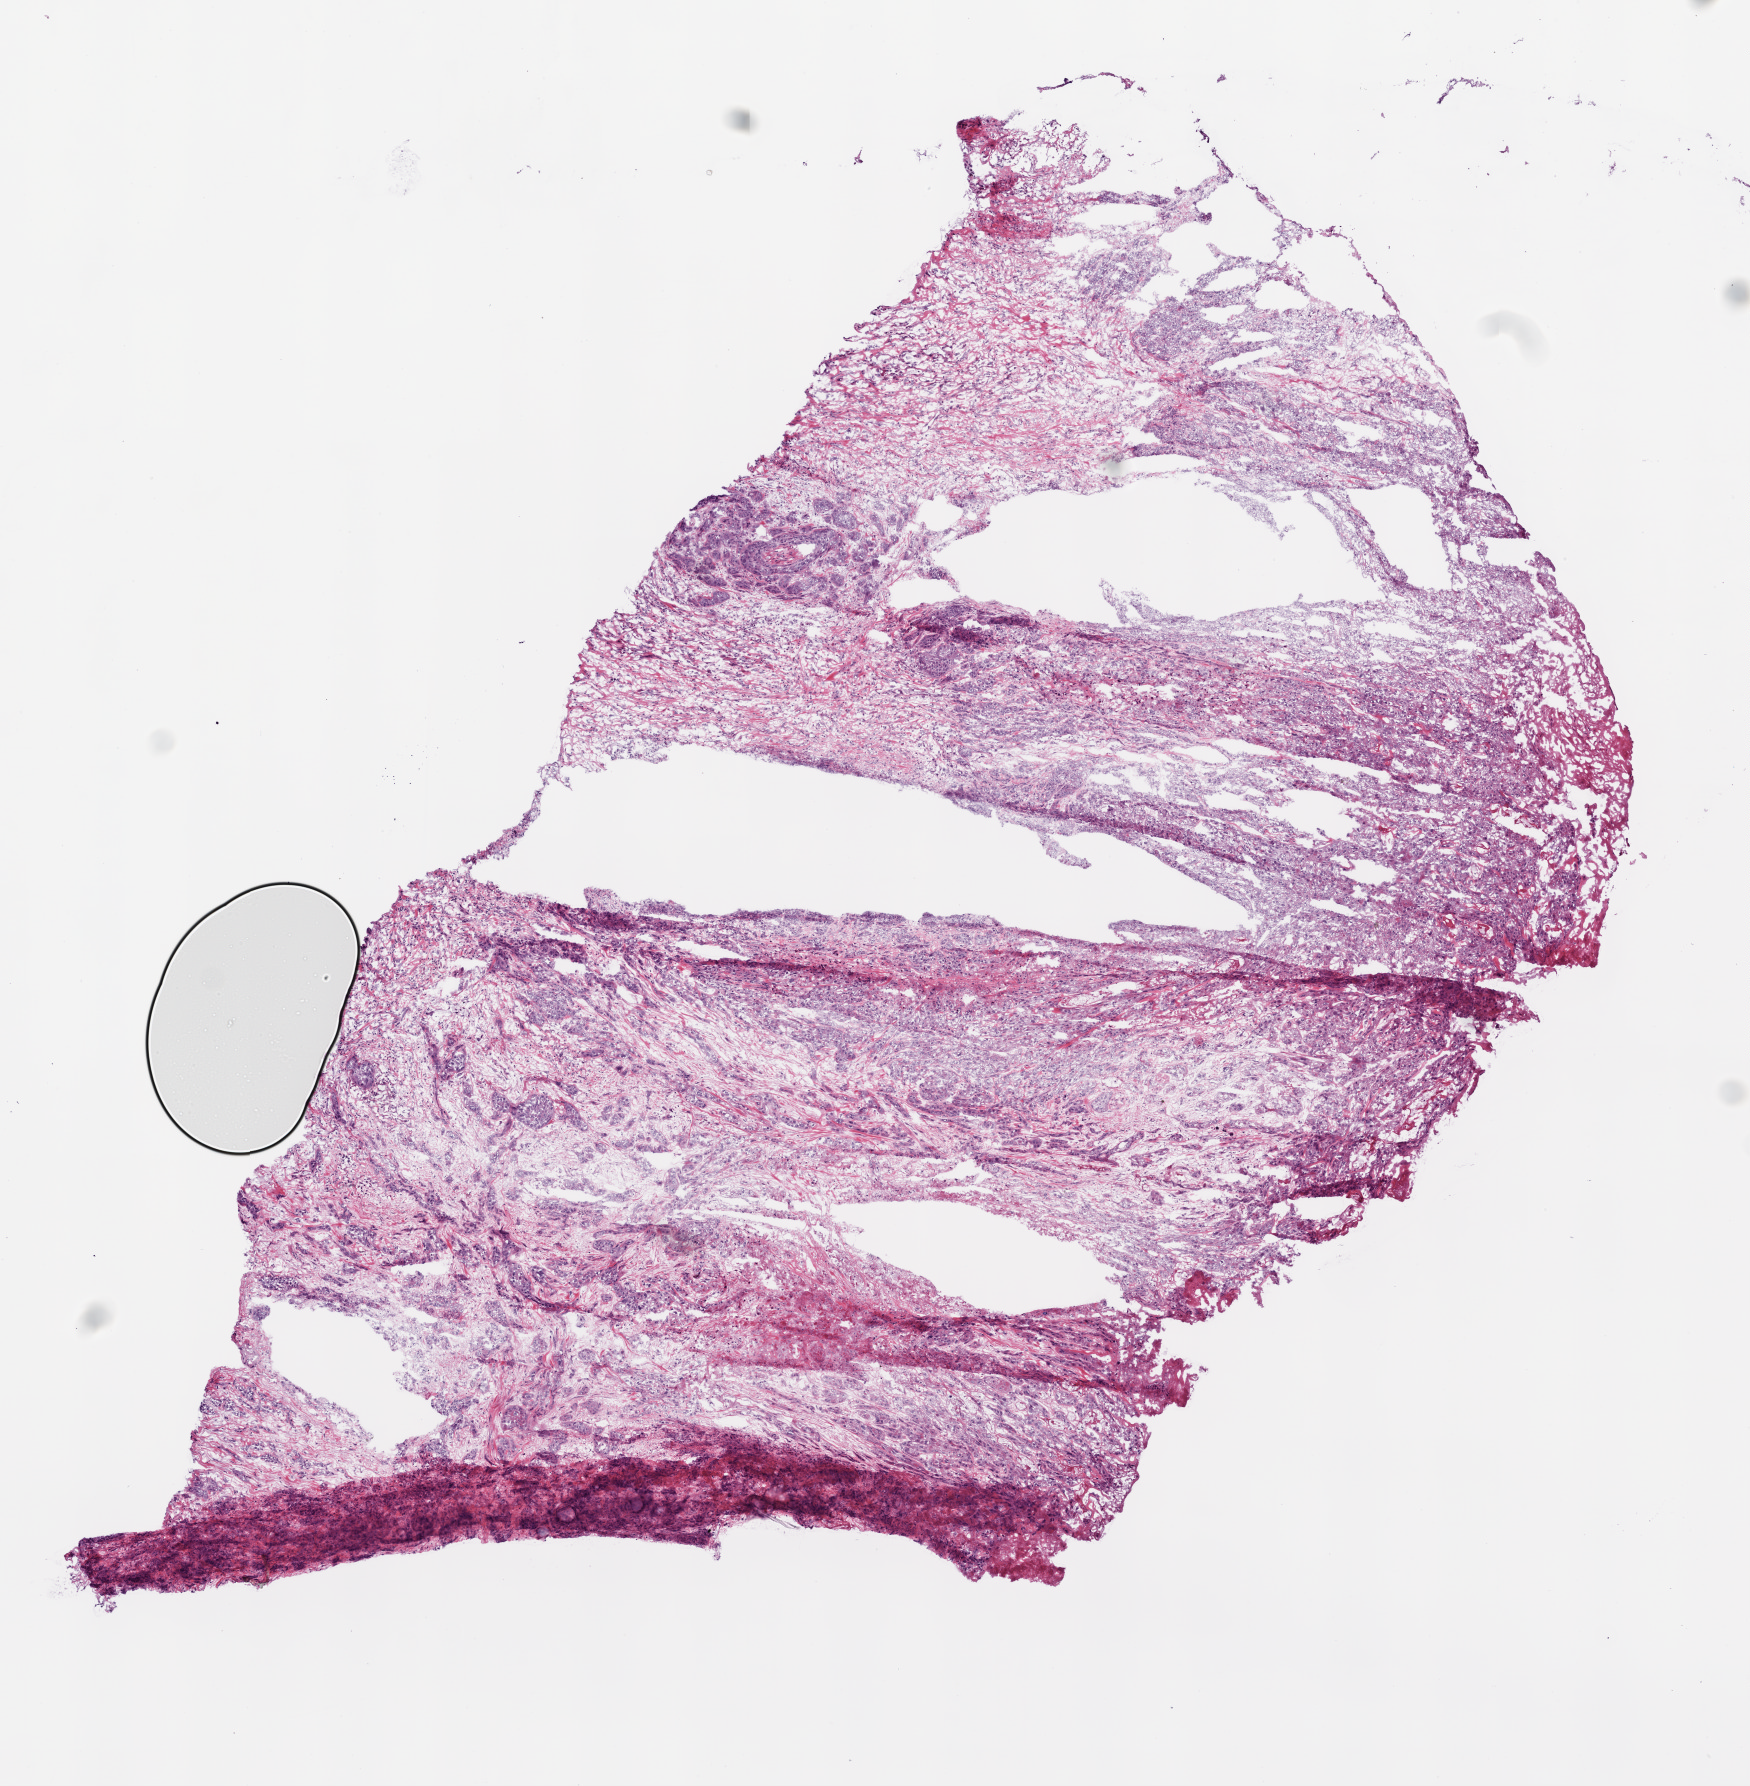
Hematoxylin and eosin (H&E) stained whole-slide image — low-resolution overview of the scanned area, about 7.0 x 7.2 mm (slide scanned at 20x). Frozen section. Primary tumour sample from the head and neck. Male patient; age at initial diagnosis 49 years. Histologic grade: G2 (moderately differentiated). Slide review estimates, as recorded: tumour cells 75%, tumour nuclei 80%, normal cells 0%, stromal cells 20%, necrosis 5%.
Lymph nodes positive (case pathology): 0 of 48 examined. AJCC pathologic stage: III. Diagnosis: Squamous cell carcinoma, NOS (tongue, NOS).